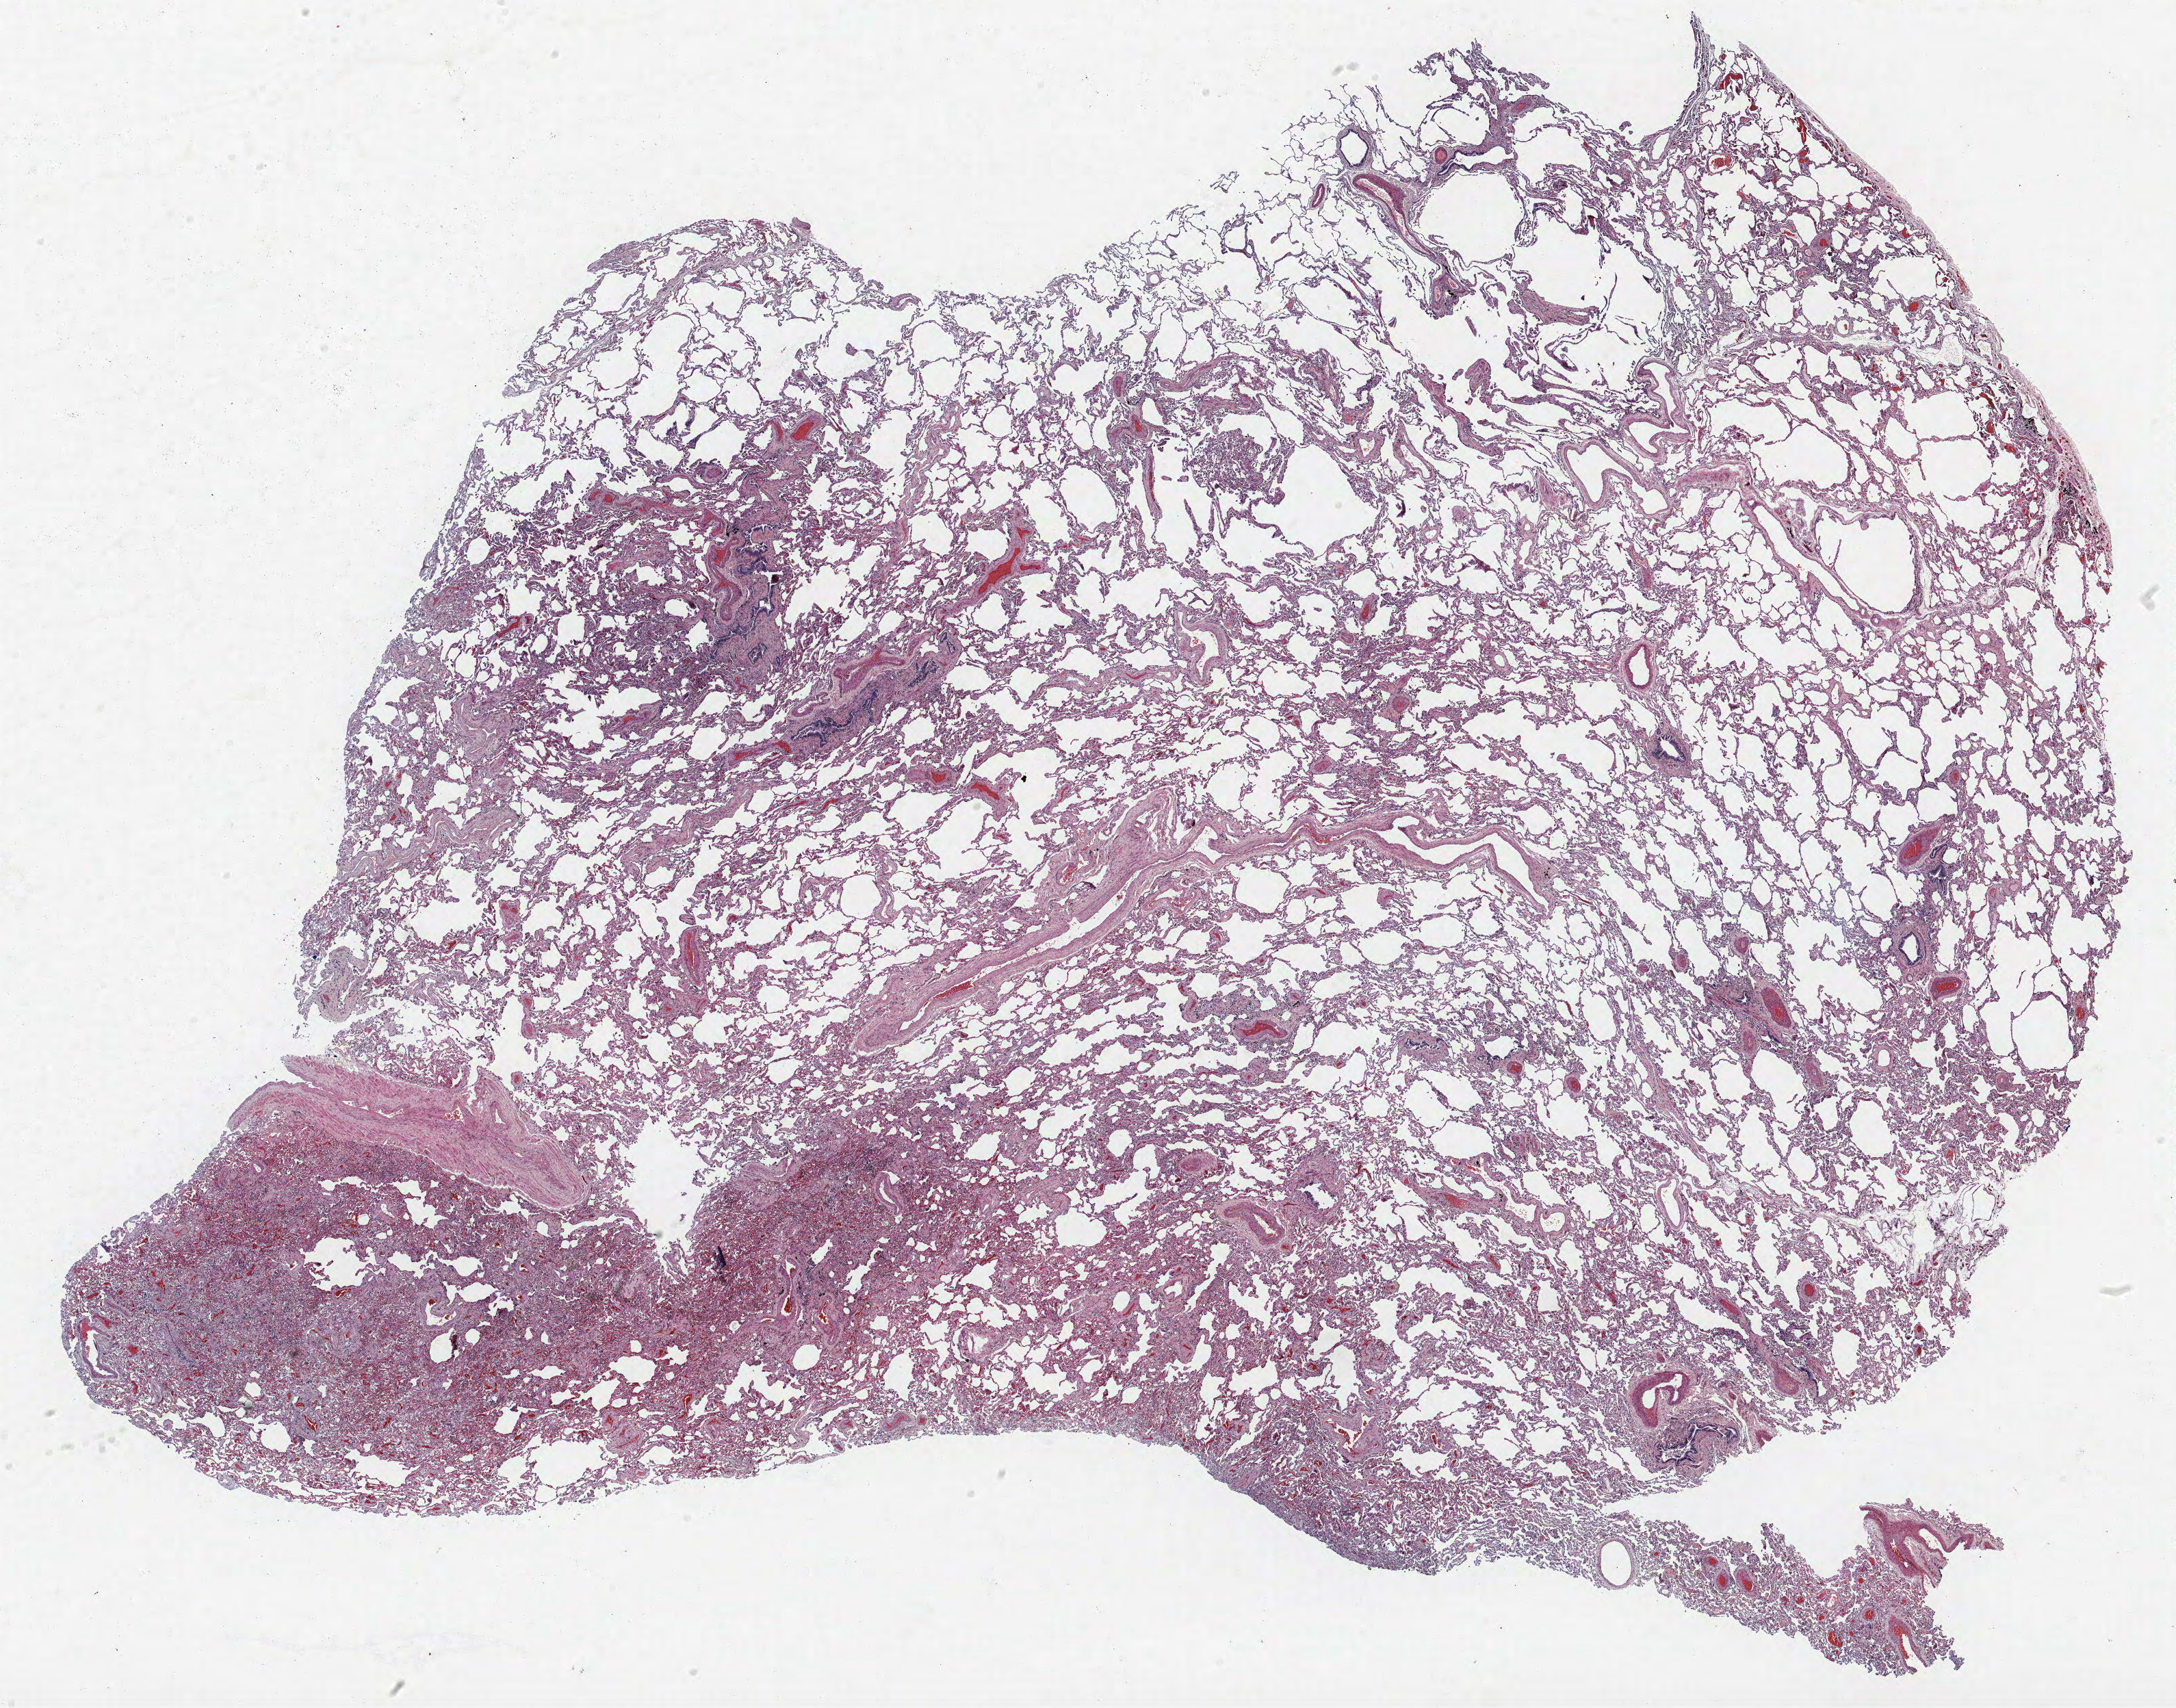
H&E-stained whole-slide image, whole scanned area (about 25.4 x 20.0 mm) shown as a low-resolution overview, formalin-fixed paraffin-embedded (FFPE) section, lung. Female patient, aged 64 at enrolment. Current smoker at enrolment.
Participant's lung-cancer diagnosis: Adenocarcinoma, NOS (ICD-O-3 8140/3).